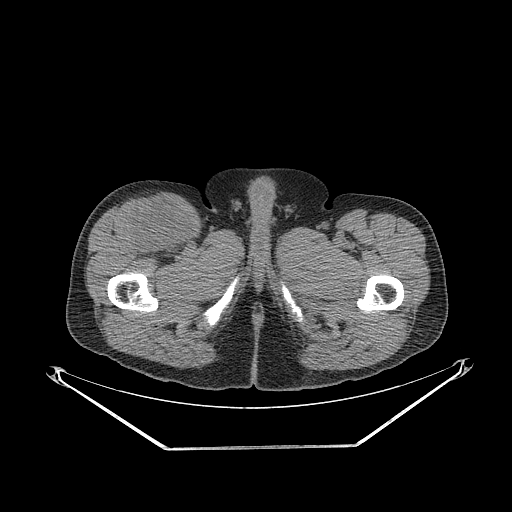
CT of an extremity soft-tissue mass (from a PET/CT study), one axial slice. Position 301 of 311 along the scan axis. Soft-tissue window (W 400 / L 40 HU). 3.75 mm slice thickness. 512 × 512 image matrix. Male patient. Case-level facts recorded for this patient, not image findings: histological type: pleiomorphic leiomyosarcoma; grade: intermediate; site of the primary tumour: right thigh.
Structures marked on this image (expert contour drawn on MRI and transferred to this co-registered scan by the dataset authors):
- gross tumour volume including surrounding oedema: bounding box [x1, y1, x2, y2] px = [128, 196, 193, 254]
- gross tumour volume (mass): [130, 203, 191, 252]